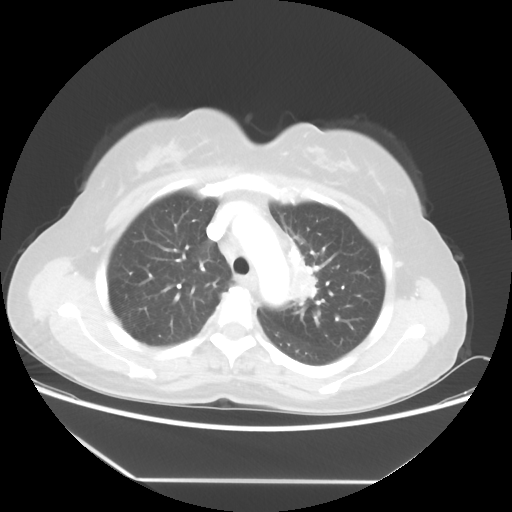
Chest CT, one axial slice. Position 39 of 52 along the scan axis. Reconstruction kernel STANDARD. 100 kVp. Lung window (W 1500 / L -600 HU). 5 mm slice thickness. 512 × 512 image matrix. Female patient, age 50 years. Case-level facts recorded for this patient, not image findings: clinical TNM (as recorded): T2 N3 M0.
Outlined on this slice (bounding box drawn by a radiologist):
- lung tumour (recorded histology: adenocarcinoma): bounding box <284,256,328,315> (left, top, right, bottom; pixels)